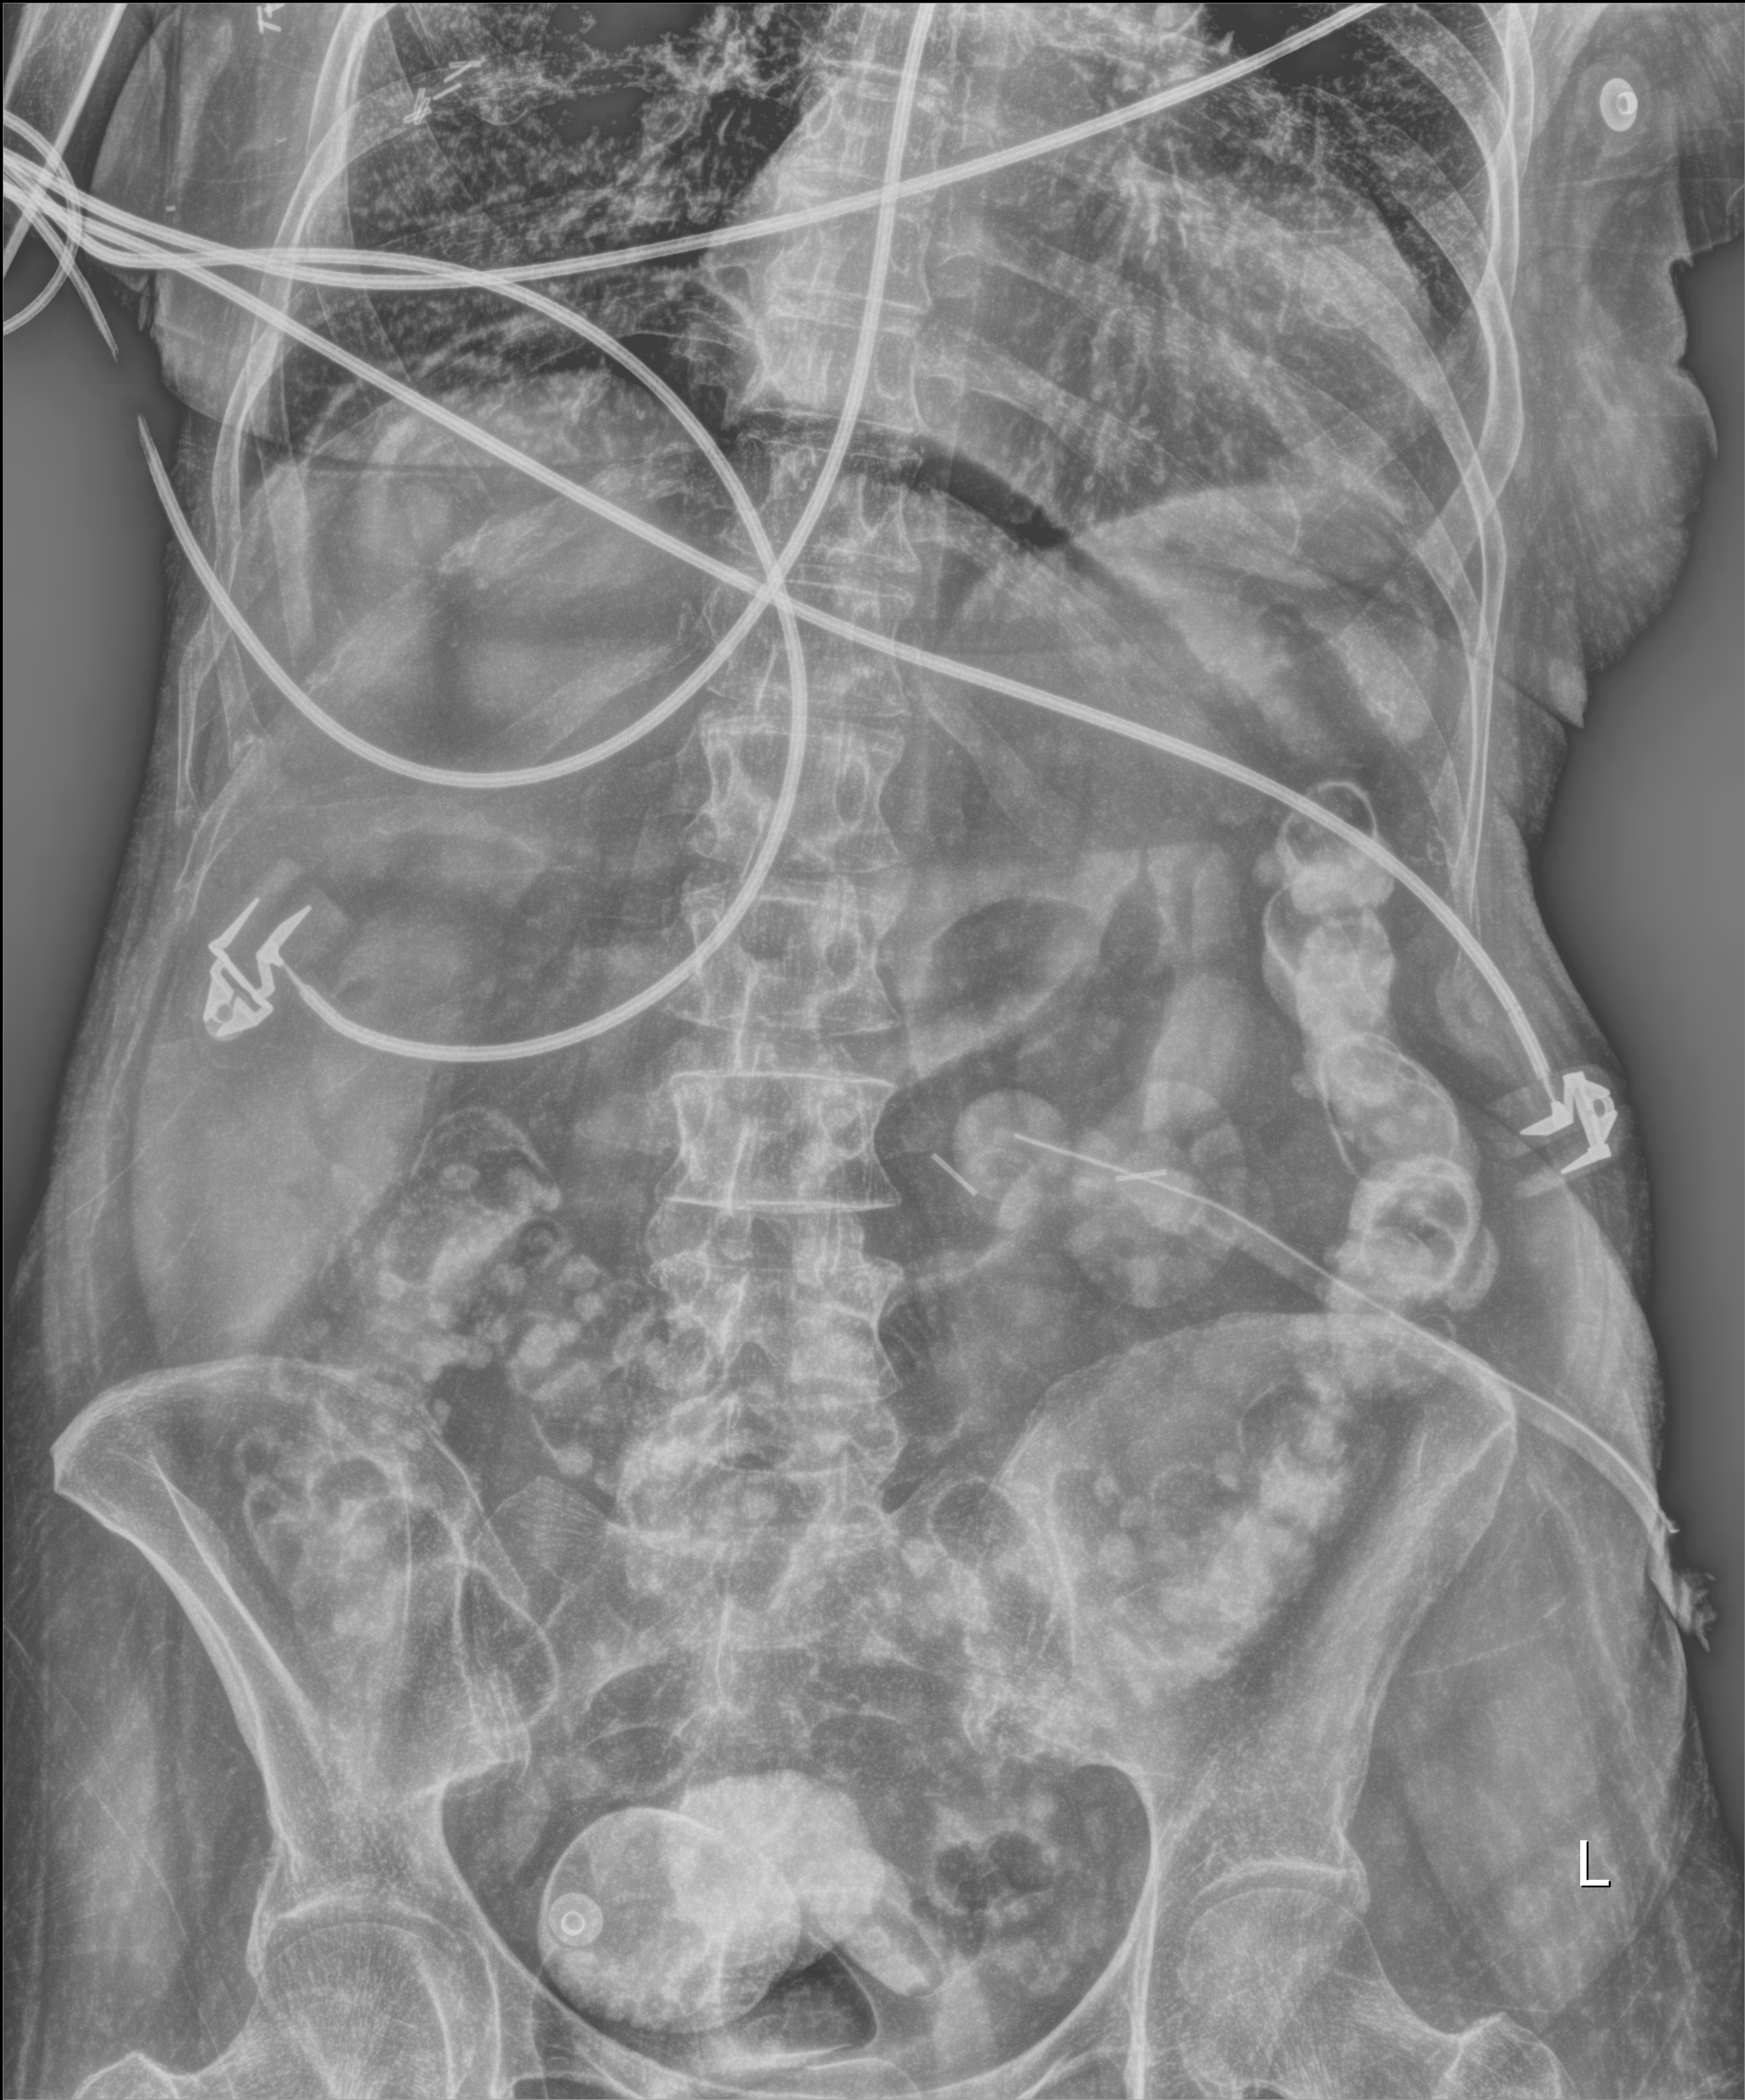
Abdomen X-ray (portable), anteroposterior (AP) projection. Female patient hospitalised with COVID-19, age 60–74 years.
Hospital-stay facts (about this admission, not read from this image; timing relative to this image not recorded): mechanically ventilated during this hospital stay: yes.